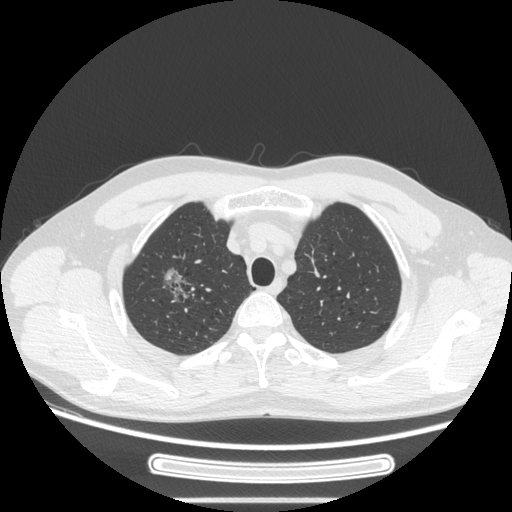
Chest CT, one axial slice. Slice 219 of 269 in the series (ordered by position). Reconstruction kernel STANDARD. Lung window (W 1500 / L -600 HU). 1.25 mm slice thickness. 512 × 512 image matrix, field of view 382 × 382 mm. Male patient, age 53 years. Case-level facts recorded for this patient, not image findings: clinical TNM (as recorded): T1c N0 M0; histopathological grade: G2.
Outlined on this slice (bounding box drawn by a radiologist):
- lung tumour (recorded histology: adenocarcinoma): box from (x=157, y=264) to (x=196, y=308) px